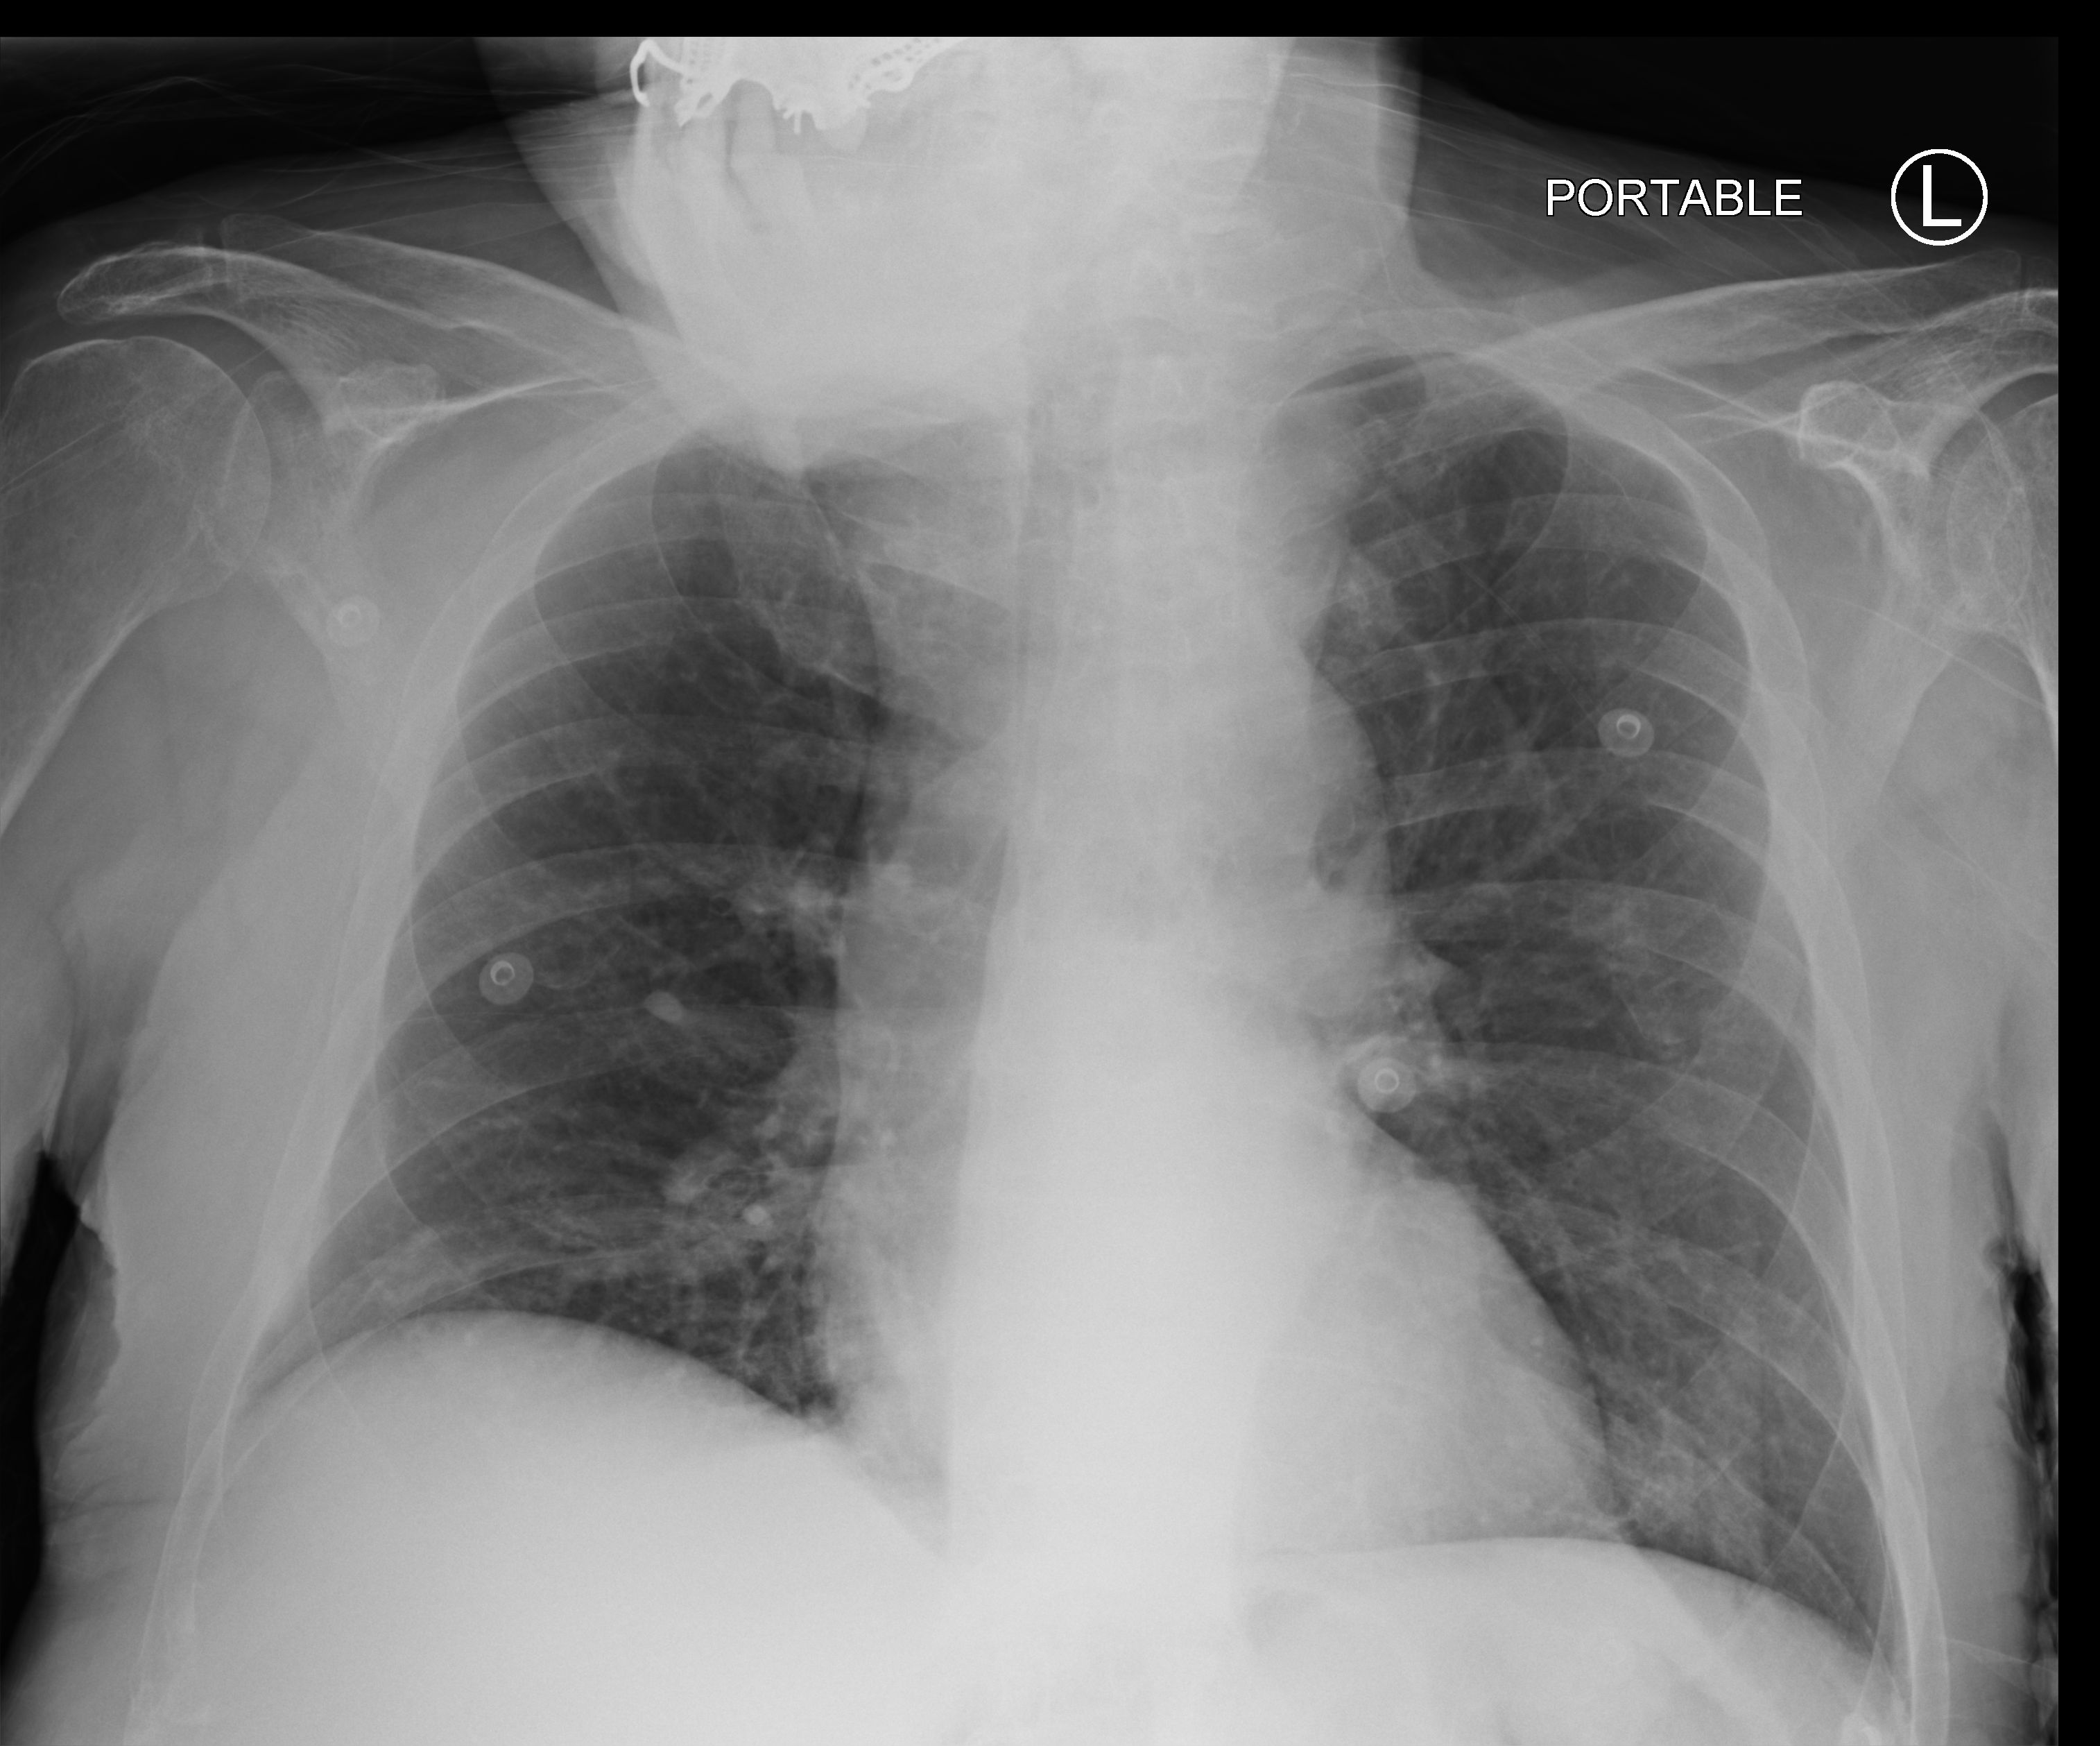
Chest X-ray (portable); anteroposterior (AP) projection. Patient hospitalised with COVID-19; male, aged 60–74 years.
From the hospital-stay record, not from the radiograph (when in the stay this image was taken is not recorded): hypertension (admission record): yes; chronic kidney disease (admission record): no; mechanically ventilated during this hospital stay: no.